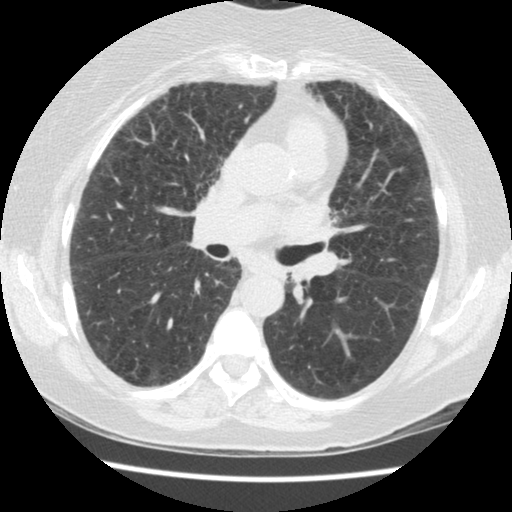
Axial slice from a low-dose chest CT screening exam. Second annual screen. Lung window (W 1500 / L -600 HU). 2.5 mm slice thickness. 120 kVp. 512 × 512 image matrix. Female participant, aged 60 years at enrolment.
• Expert-annotated lung lesion, box from (x=267, y=258) to (x=316, y=304) px.
• Reader record for this screening exam (exam-level; its link to the box is not recorded): non-calcified nodule or mass ≥4 mm, left lower lobe, 5 × 4 mm, smooth margins, soft tissue attenuation, pre-existing on the prior screen: yes; interval growth: no.
• Official screen result: positive, no significant change: stable abnormalities potentially related to lung cancer, unchanged since the prior screening exam.
• Lung cancer was diagnosed 423 days after this screen: small cell carcinoma, NOS, left lower lobe, undifferentiated (G4), stage IV (AJCC 6th edition), 69 mm at pathology.